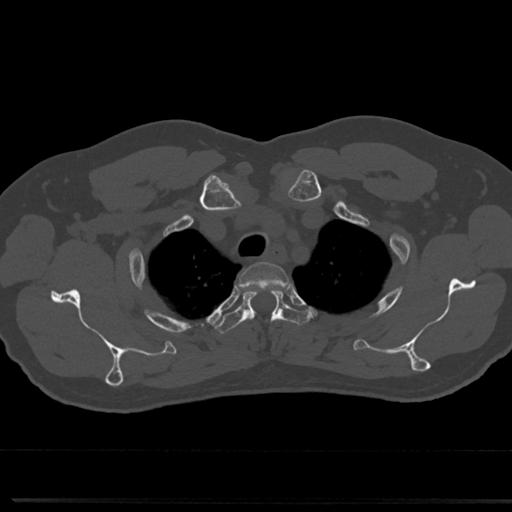
CT including the spine, one axial slice; slice 606 of 817 in the series (ordered by position); reconstruction kernel Br40s/3; 120 kVp; bone window (W 1800 / L 400 HU); 512 × 512 image matrix, field of view 355 × 355 mm. Patient: male, 61 years. From the clinical record (not read from this slice): primary cancer: prostate.
Outlined on this slice (semi-automatically segmented with operator editing):
- T2 vertebra: bounding box [x1, y1, x2, y2] px = [240, 262, 288, 283]
- T3 vertebra: [216, 285, 303, 332]